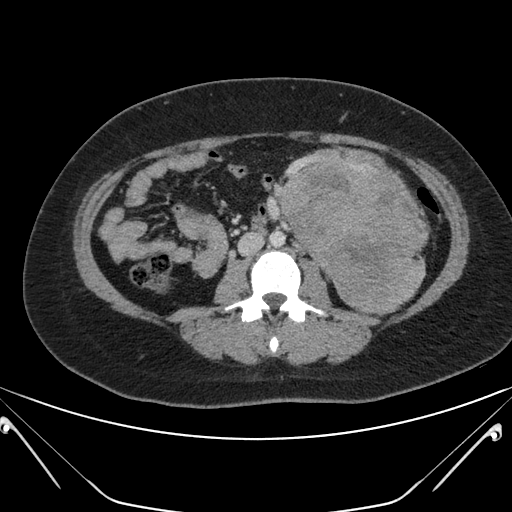
Contrast-enhanced abdominal CT, one axial slice. Slice 92 of 168 in the series (ordered by position). 120 kVp. Intravenous contrast given. Soft-tissue window (W 400 / L 40 HU). 3 mm slice thickness. 512 × 512 image matrix, field of view 394 × 394 mm. Female patient, age 26 years. Case-level facts recorded for this patient, not image findings: diagnosis: adrenocortical carcinoma; tumour side: left adrenal; tumour size at pathology: 28 cm; Ki-67 index: 20 %; stage (as recorded): 2.
Outlined on this slice (semi-automatically segmented with operator editing):
- mass: box from (x=282, y=161) to (x=425, y=311) px